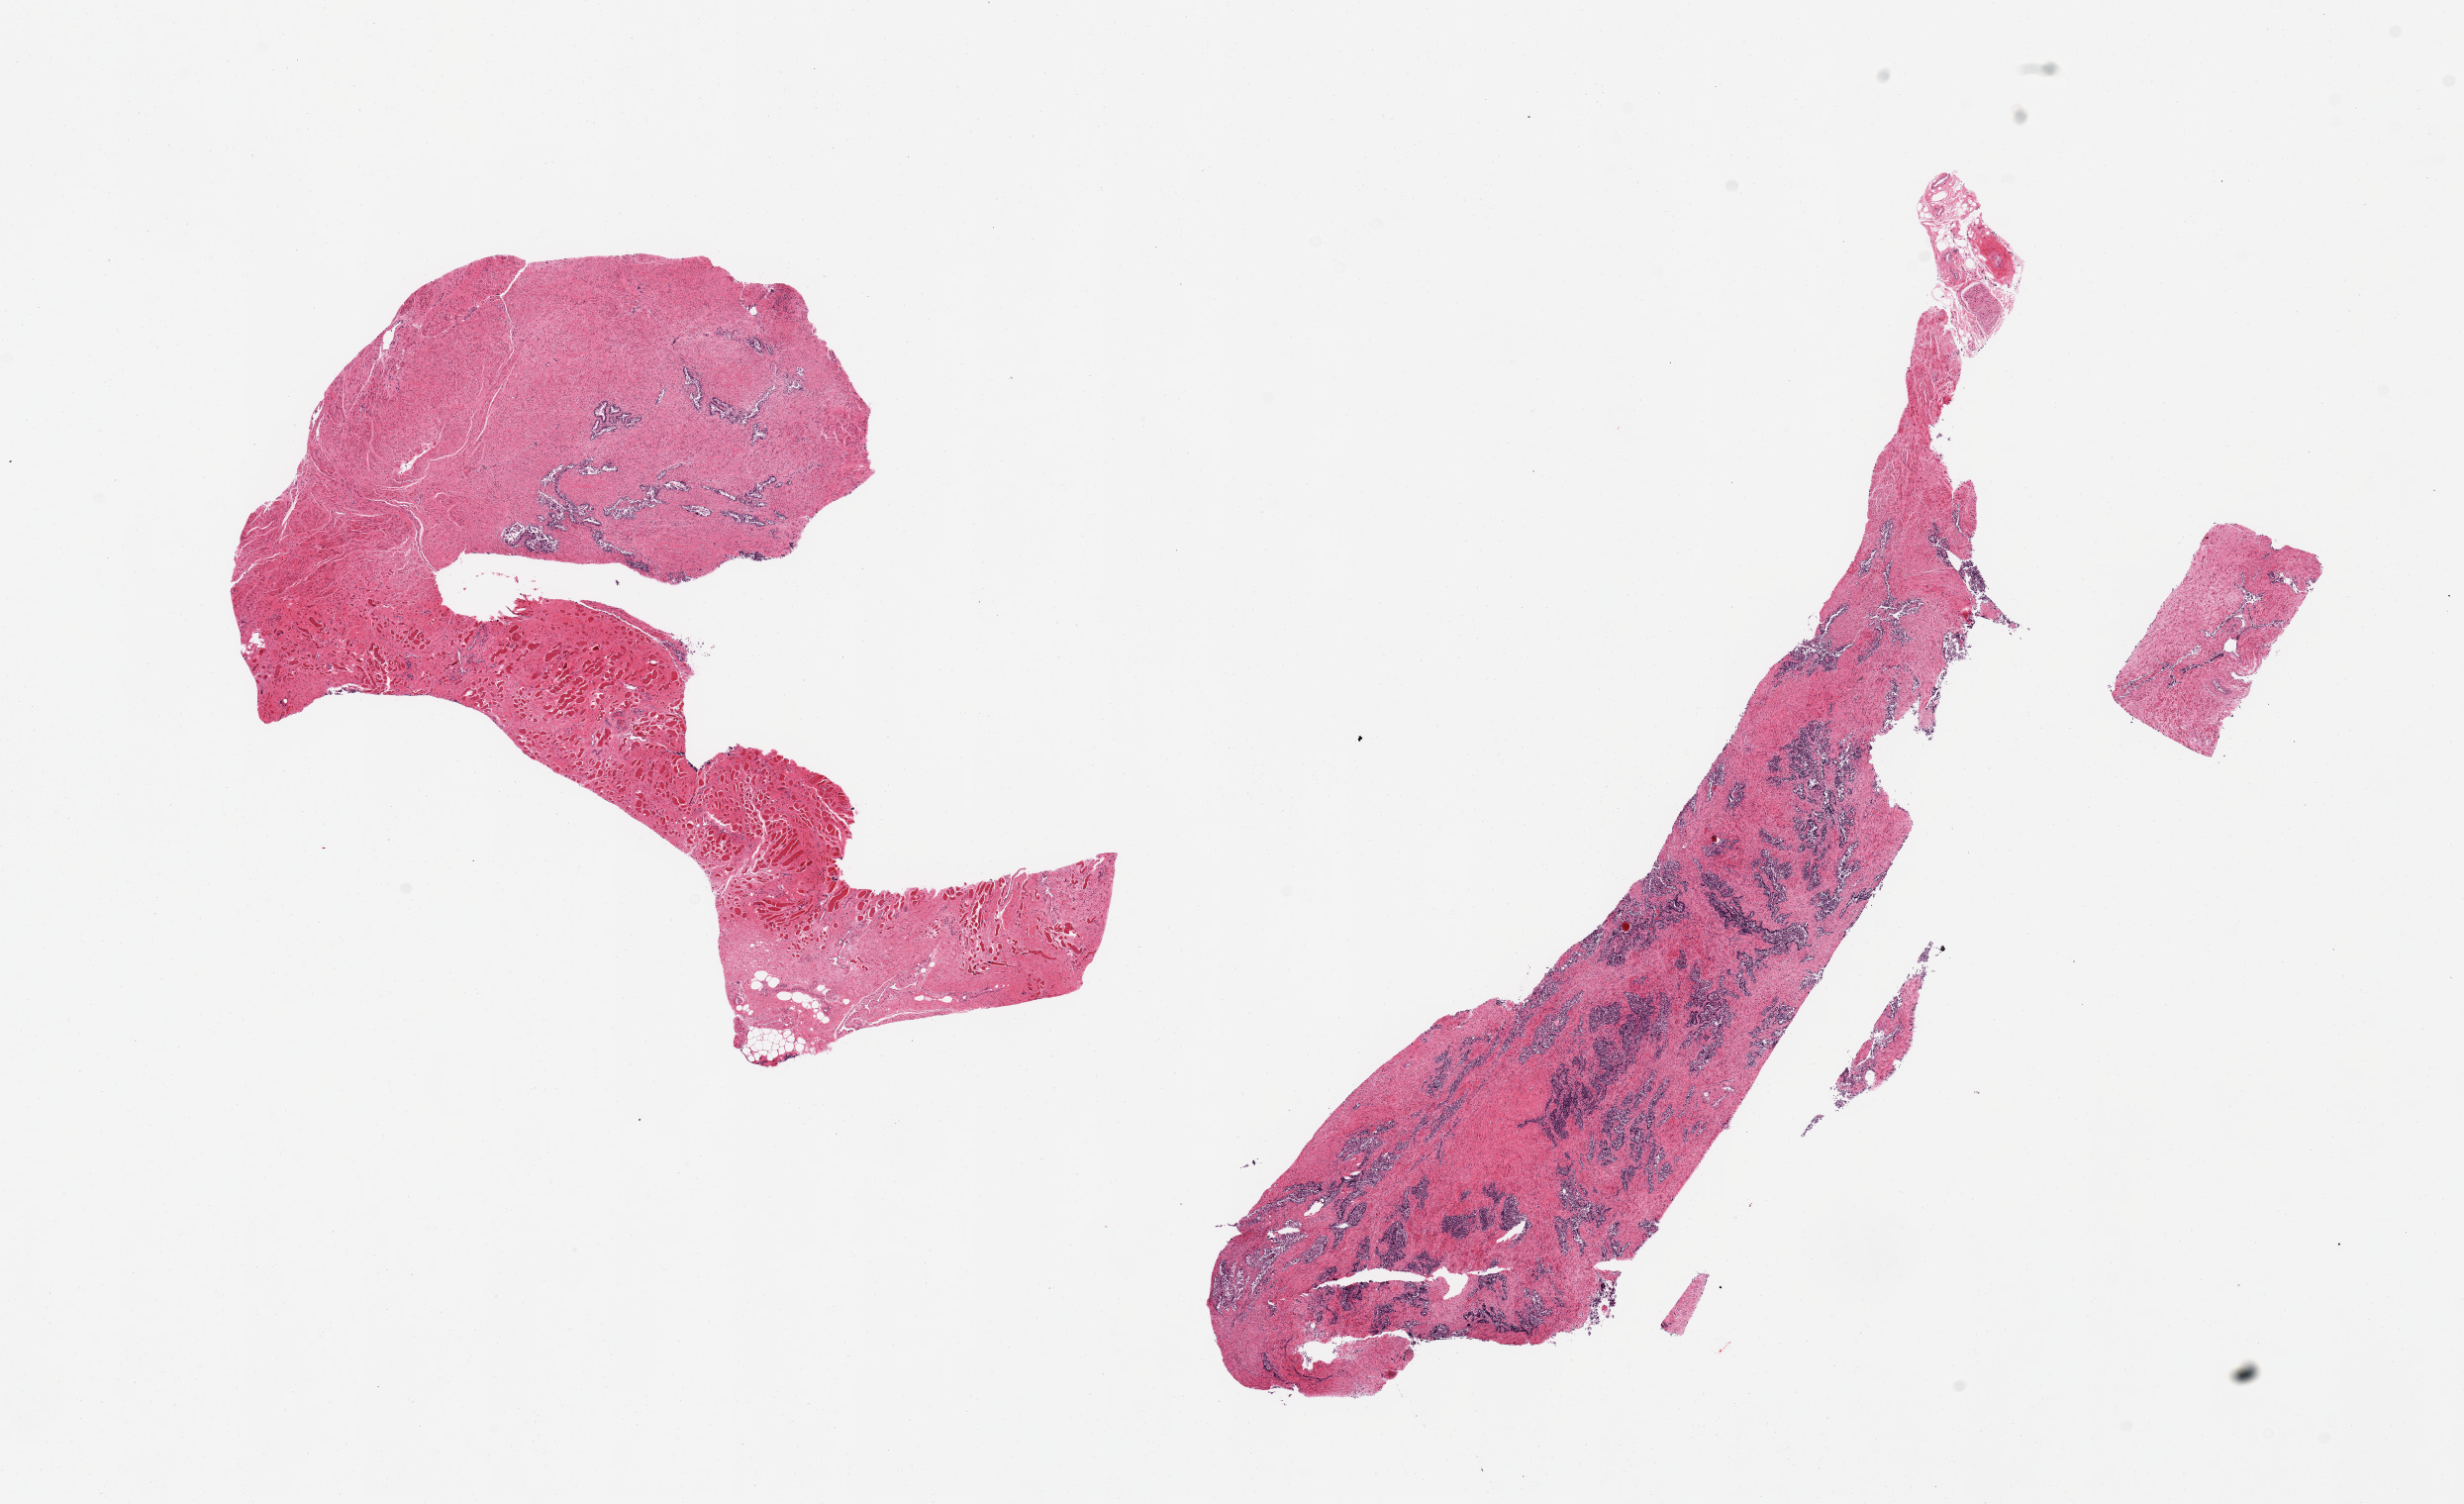
Hematoxylin and eosin (H&E) whole-slide image — low-resolution overview of the scanned area, about 19.7 x 12.0 mm (acquisition: 20x scan); PAXgene-fixed paraffin-embedded (PFPE) section; section of prostate (target tissue); donor tissue sample.
Review note (as recorded): 3 pieces; glands = 3; stroma = 1.